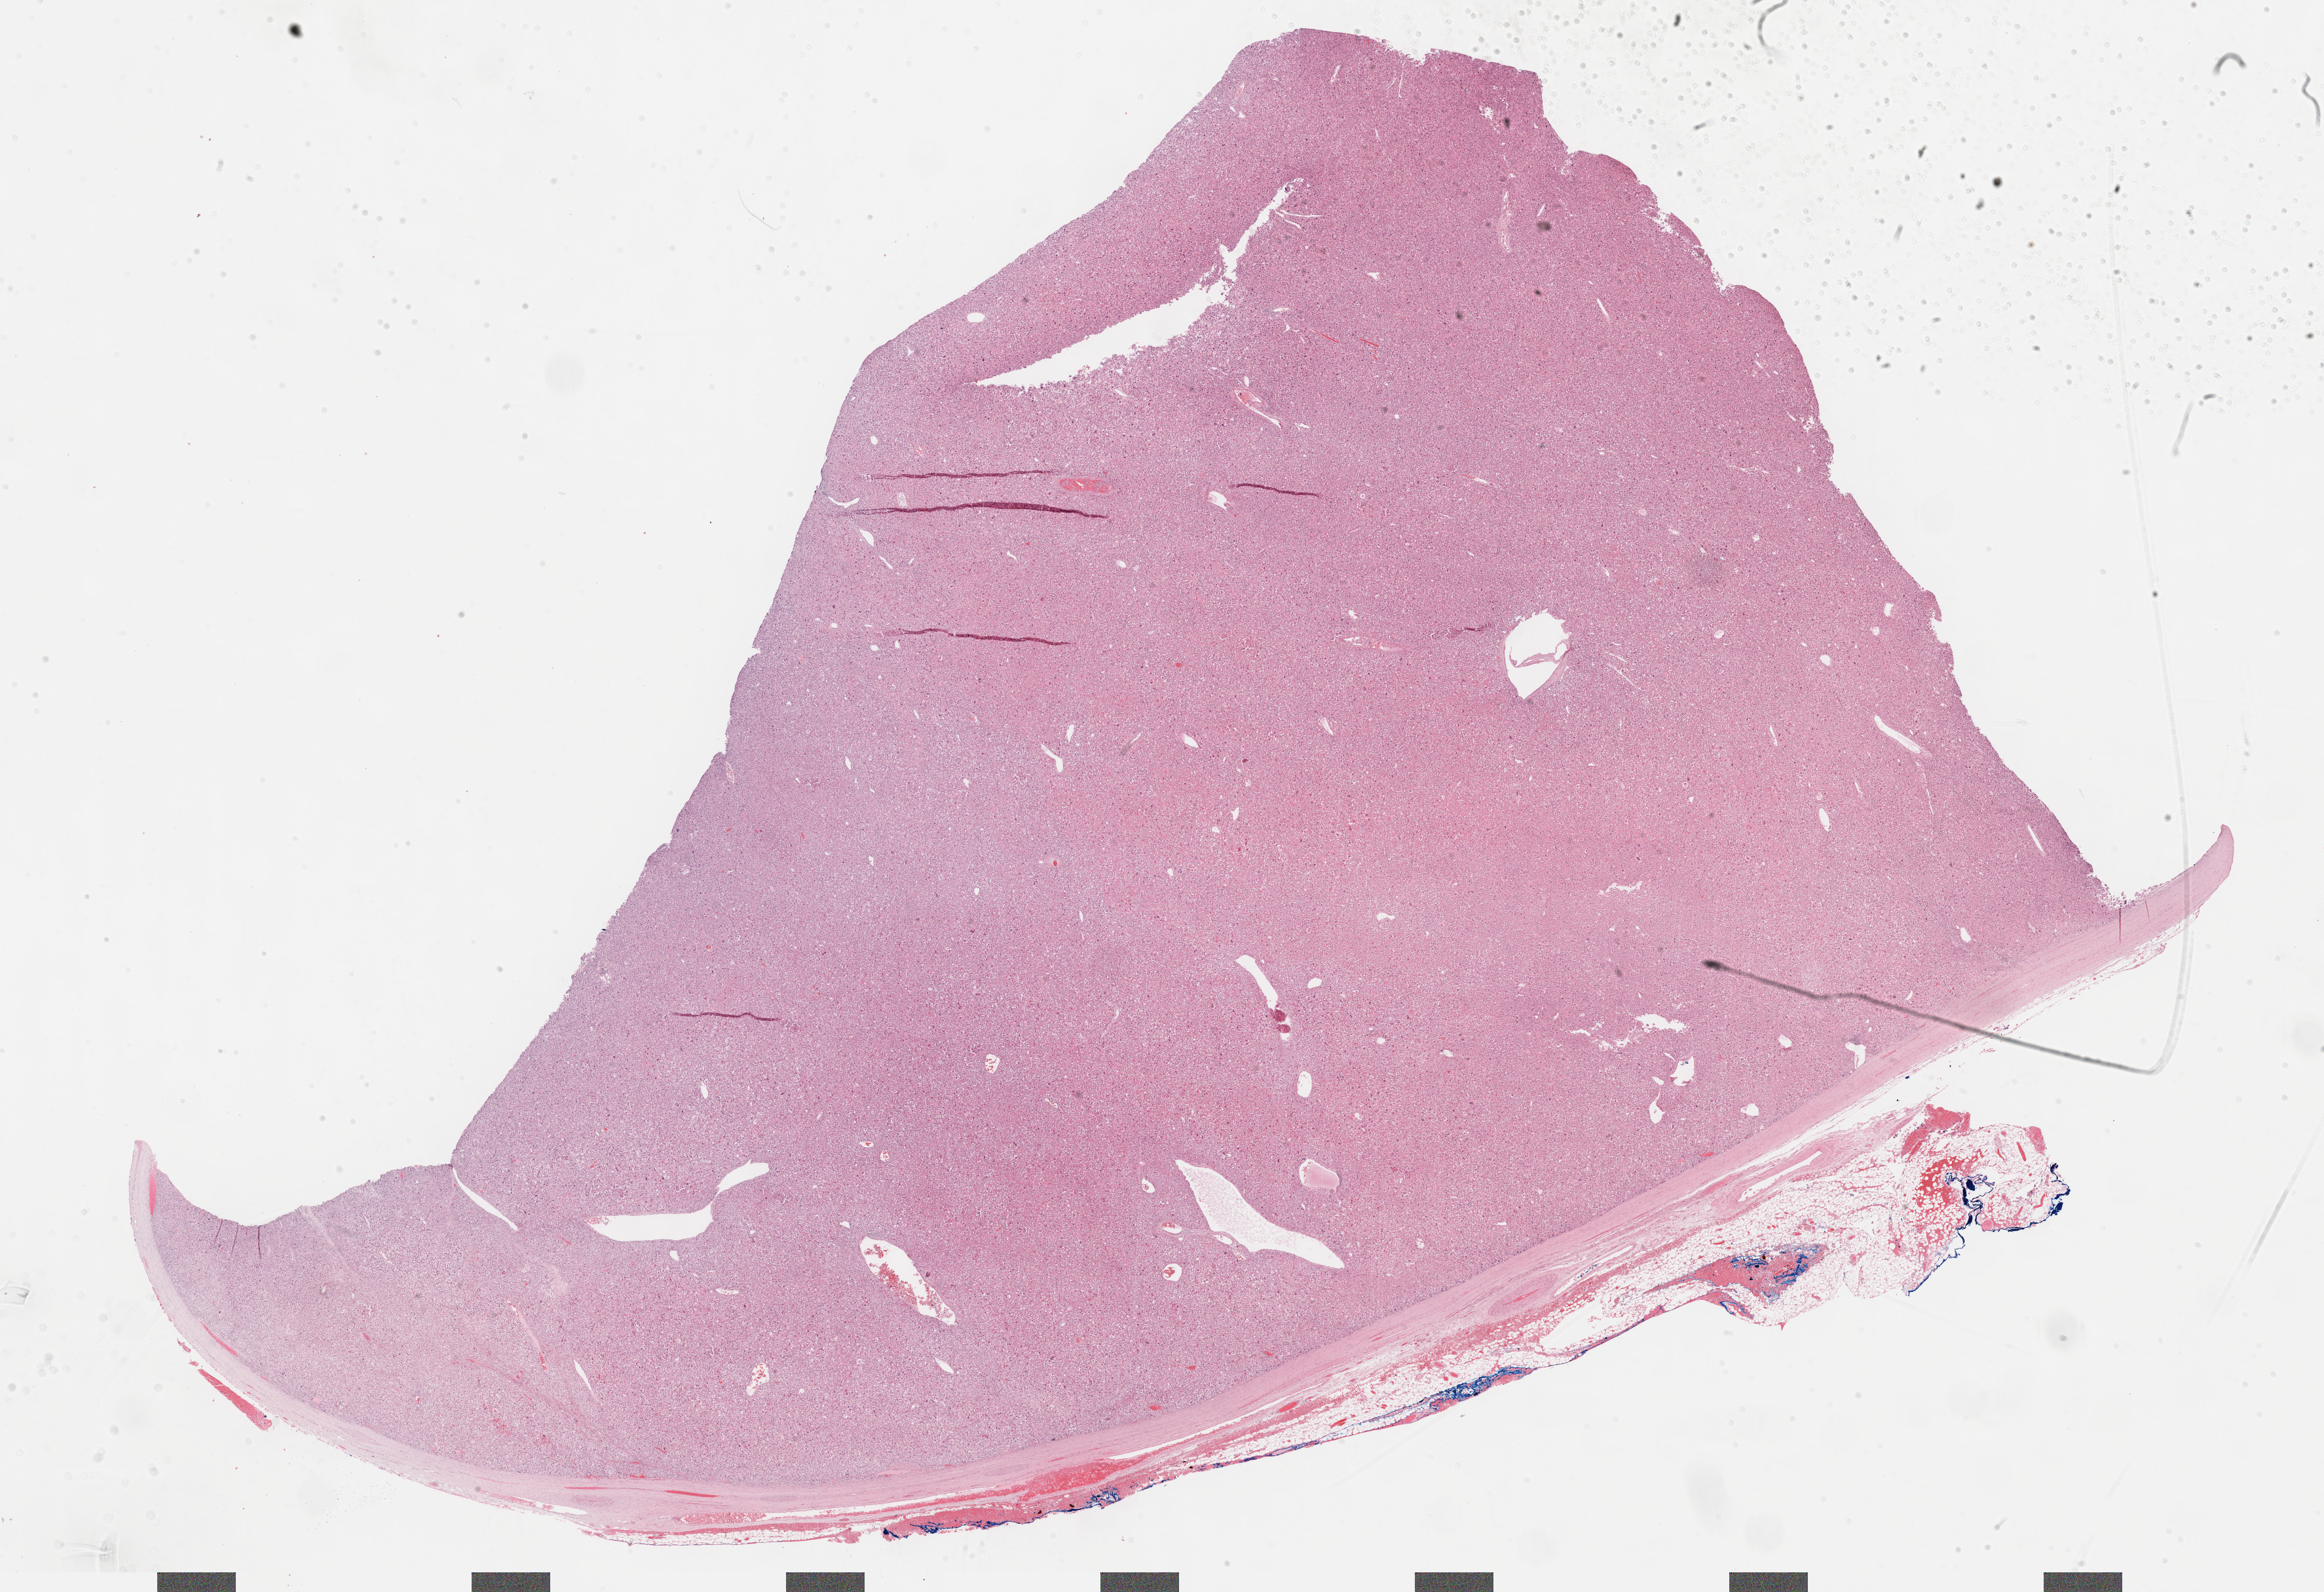
H&E whole-slide image, low-resolution overview of the scanned area, about 28.7 x 19.7 mm (from a 40x scan), formalin-fixed paraffin-embedded (FFPE) diagnostic section, primary tumour sample from the adrenal cortex. Female patient; age at initial diagnosis 64 years.
Laterality: right. Pathologic diagnosis: Adrenal cortical carcinoma (cortex of adrenal gland).